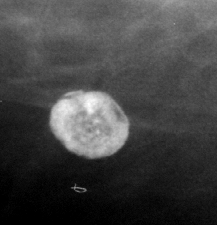
Cropped region of a digitized screen-film mammogram centred on a radiologist-marked abnormality, right breast, MLO view, BI-RADS breast density category 3 (scale 1–4).
Calcifications, morphology round and regular / eggshell; BI-RADS assessment category 2; subtlety rating 3 on a 1 (subtle) to 5 (obvious) scale; benign without callback (not worked up further).